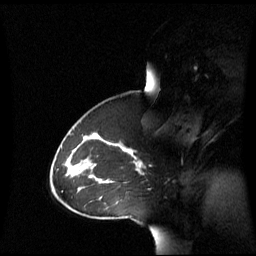
Breast MRI (dynamic contrast-enhanced), one sagittal slice; slice 41 of 60 in the series (ordered by position); dynamic contrast-enhanced series, image 2 of 3 at this slice position (ordered by acquisition); 1.5 T; TE 4.2 ms, TR 8.4 ms; 256 × 256 image matrix, field of view 270 × 270 mm. Female patient, age 43 years. Case-level facts recorded for this patient, not image findings: setting: breast cancer imaged before/during neoadjuvant chemotherapy; receptor status: triple-negative.
Annotated regions visible in this slice (semi-automatically segmented with operator editing):
- analysis volume of interest (the breast-tissue region the enhancement analysis was run in; not a lesion): bounding box <69,137,143,198> (left, top, right, bottom; pixels)
- tumour enhancement mask (voxels above the 70 % enhancement threshold inside the analysis volume of interest): <121,146,142,172>